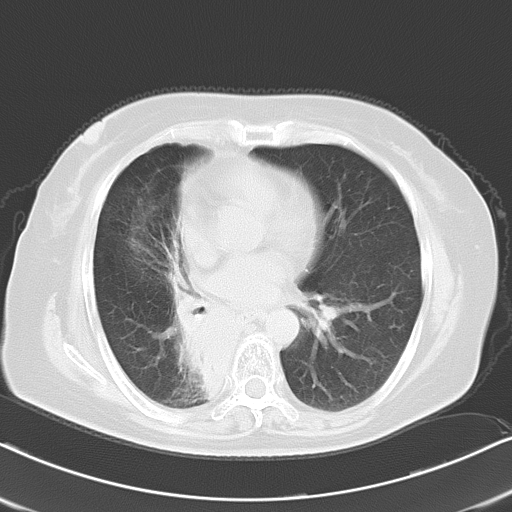
Chest CT, one axial slice; position 10 of 21 along the scan axis; reconstruction kernel B70f; lung window (W 1500 / L -600 HU); 10 mm slice thickness; 512 × 512 image matrix, field of view 326 × 326 mm. Patient: female, 61 years. From the clinical record (not read from this slice): clinical TNM (as recorded): T1b N0 M1b.
Structures marked on this image (rectangle marked by the reading radiologist):
- lung tumour (recorded histology: squamous cell carcinoma): box from (x=160, y=270) to (x=251, y=422) px